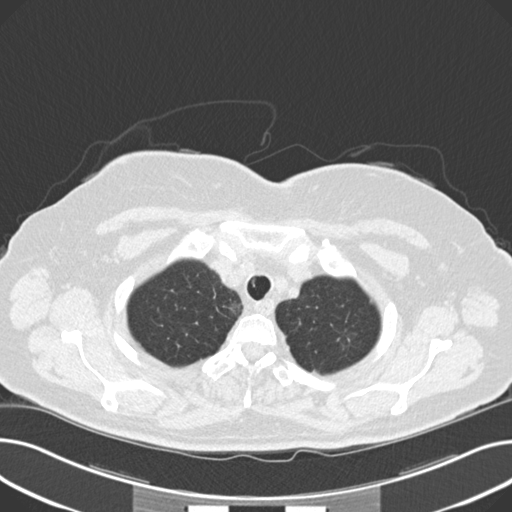
Low-dose screening chest CT, axial slice, third screening round (two years after baseline), lung window (W 1500 / L -600 HU), 2 mm slice thickness, standard (soft-tissue) reconstruction kernel (B30f), 120 kVp, slice 33 of 203 in the series. Female, age 60 years at enrolment. Current smoker at enrolment.
- Lesion marked by an expert reader, box from (x=335, y=322) to (x=379, y=365) px.
- The screening reader recorded 8 non-calcified nodules or masses ≥4 mm on this exam (right upper lobe, lingula, lingula, right middle lobe, right lower lobe, left lower lobe, left lower lobe, left lower lobe); which of them this box marks is not recorded.